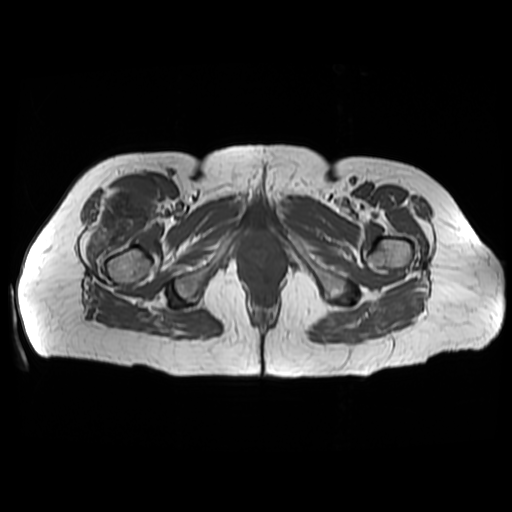
MRI of an extremity soft-tissue mass, one axial slice. Position 39 of 48 along the scan axis. 6 mm slice thickness. 512 × 512 image matrix, field of view 440 × 440 mm. Female patient. From the clinical record (not read from this slice): histological type: pleiomorphic undifferentiated sarcoma; grade: high; site of the primary tumour: right quadricep.
Annotated regions visible in this slice (manually delineated by an expert):
- gross tumour volume including surrounding oedema: box from (x=86, y=183) to (x=162, y=264) px
- gross tumour volume (mass): (x=100, y=183)–(x=162, y=237)